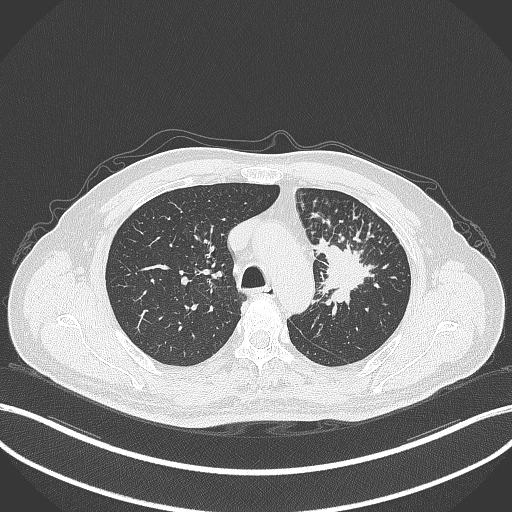
Chest CT, one axial slice; position 260 of 386 along the scan axis; lung window (W 1500 / L -600 HU); 512 × 512 image matrix, field of view 400 × 400 mm. Male patient, age 69 years. Case-level facts recorded for this patient, not image findings: clinical TNM (as recorded): T2a N2 M0.
Structures marked on this image (bounding box drawn by a radiologist):
- lung tumour (recorded histology: adenocarcinoma): bounding box <315,236,380,307> (left, top, right, bottom; pixels)